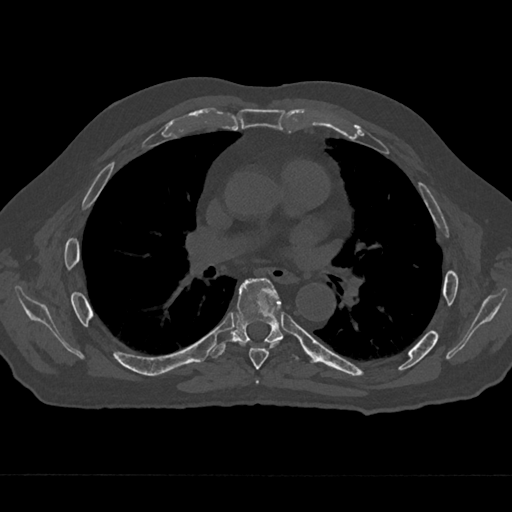
CT including the spine, one axial slice. Position 396 of 797 along the scan axis. Reconstruction kernel Br40s/3. Bone window (W 1800 / L 400 HU). 0.5 mm slice thickness. 512 × 512 image matrix, field of view 377 × 377 mm. Patient: male, 75 years. Case-level facts recorded for this patient, not image findings: primary cancer: renal; vertebrae with lytic lesions (as recorded): T4.
Annotated regions visible in this slice (semi-automatically segmented with operator editing):
- T5 vertebra: bounding box <256,379,259,384> (left, top, right, bottom; pixels)
- T6 vertebra: <239,342,279,370>
- T7 vertebra: <209,278,297,359>